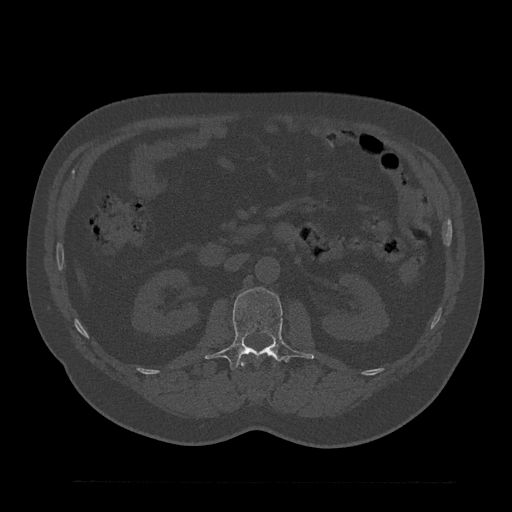
CT including the spine, one axial slice; position 110 of 797 along the scan axis; 120 kVp; bone window (W 1800 / L 400 HU); 0.5 mm slice thickness; 512 × 512 image matrix, field of view 430 × 430 mm. Male patient, age 61 years. Case-level facts recorded for this patient, not image findings: primary cancer: prostate.
Annotated regions visible in this slice (semi-automatically segmented with operator editing):
- L1 vertebra: box from (x=241, y=352) to (x=274, y=367) px
- L2 vertebra: (x=206, y=288)–(x=314, y=371)